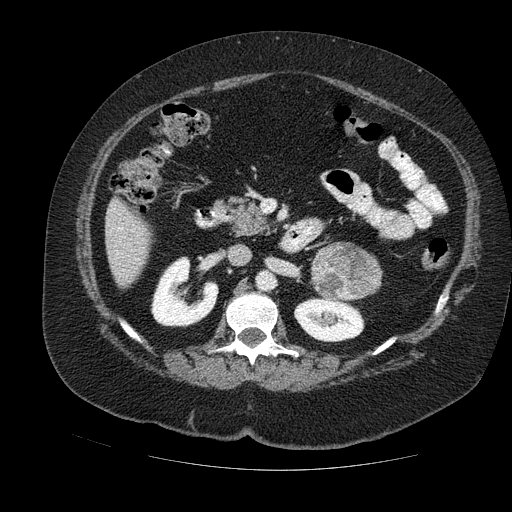
Contrast-enhanced abdominal CT, one axial slice; slice 59 of 121 in the series (ordered by position); soft-tissue window (W 400 / L 40 HU); 512 × 512 image matrix, field of view 420 × 420 mm. Female patient. Case-level facts recorded for this patient, not image findings: diagnosis: adrenocortical carcinoma; tumour side: left adrenal; tumour size at pathology: 8 cm; Ki-67 index: 7 %; stage (as recorded): 2.
Annotated regions visible in this slice (semi-automatic segmentation, software-assisted and operator-edited):
- mass: box from (x=311, y=245) to (x=378, y=299) px